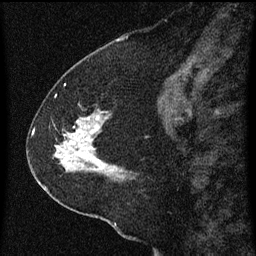
Breast MRI (dynamic contrast-enhanced), one sagittal slice; slice 27 of 60 in the series (ordered by position); dynamic contrast-enhanced series, image 2 of 3 at this slice position (ordered by acquisition); 1.5 T; TE 4.2 ms, TR 8 ms; 2 mm slice thickness; 256 × 256 image matrix, field of view 180 × 180 mm. Patient: female, 47 years.
Structures marked on this image (semi-automatically segmented with operator editing):
- analysis volume of interest (the breast-tissue region the enhancement analysis was run in; not a lesion): bounding box [x1, y1, x2, y2] px = [36, 98, 136, 213]
- tumour enhancement mask (voxels above the 70 % enhancement threshold inside the analysis volume of interest): [54, 116, 118, 177]